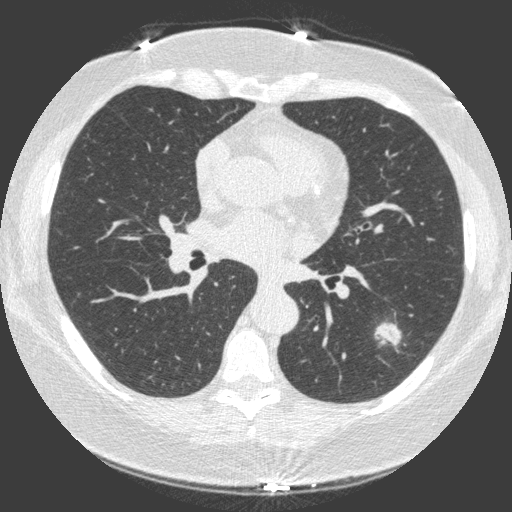
Low-dose screening chest CT, one axial slice. Position 84 of 149 along the scan axis. Lung window (W 1500 / L -600 HU). 1 mm slice thickness. 512 × 512 image matrix, field of view 330 × 330 mm.
Annotated regions visible in this slice (manually delineated by an expert):
- lesion 1 (tumor, lower lobe of left lung): bounding box <375,323,401,351> (left, top, right, bottom; pixels)